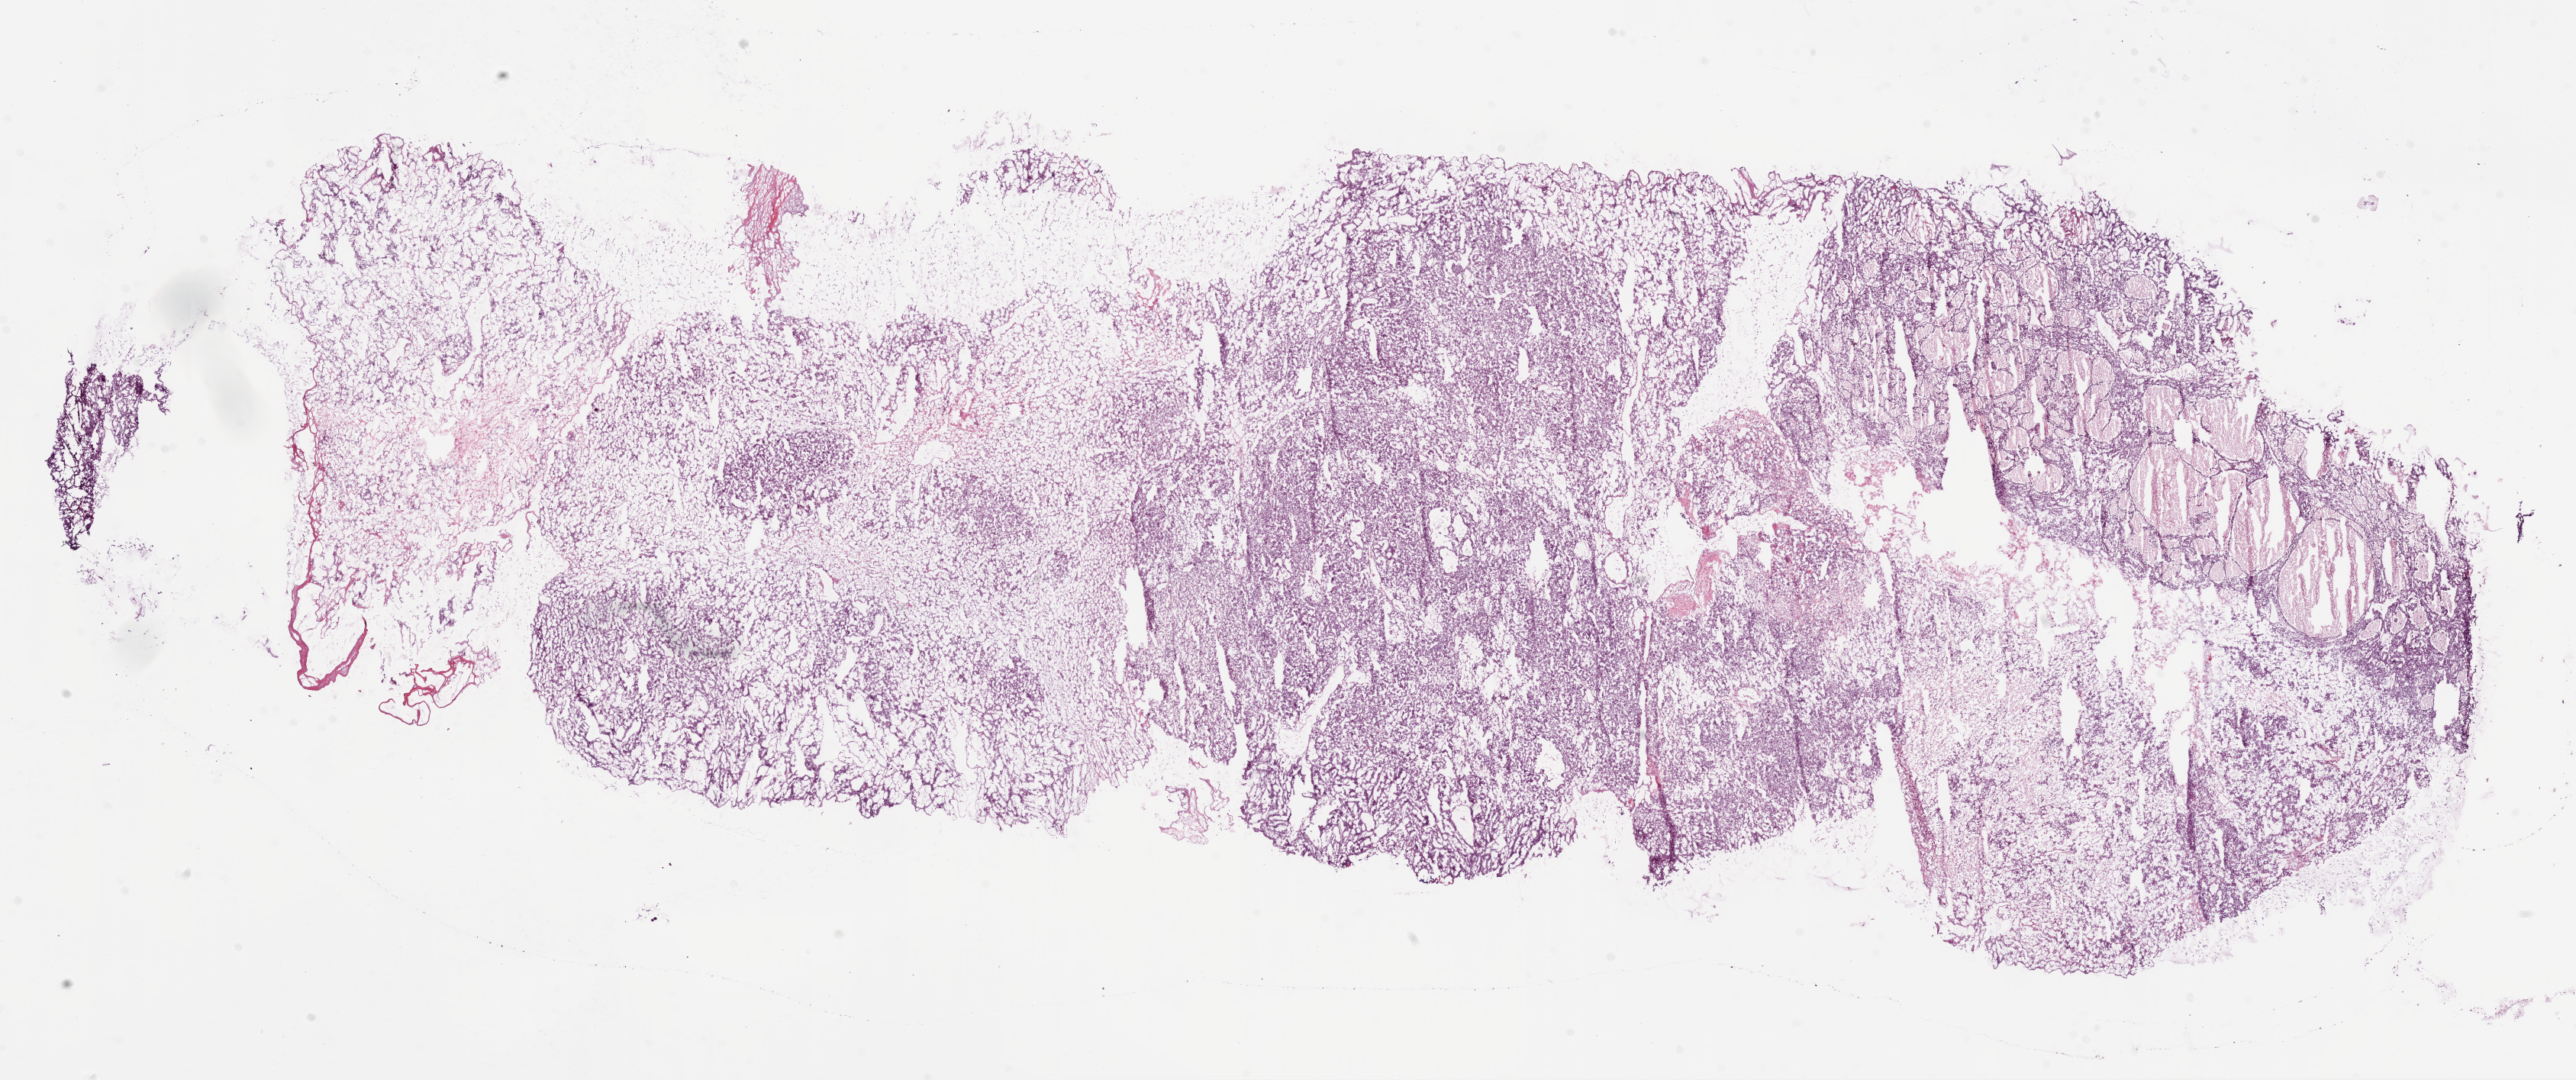
Digitized H&E tissue section (whole slide) — whole scanned area (about 27.1 x 11.4 mm) shown as a low-resolution overview; frozen section; primary tumour sample from the kidney. Male patient; age at initial diagnosis 58 years. Histologic grade: G3 (poorly differentiated). Slide review estimates, as recorded: tumour cells 85%, tumour nuclei 85%, normal cells 0%, stromal cells 15%, necrosis 0%.
* diagnosis: Clear cell adenocarcinoma, NOS
* AJCC pathologic stage: III (7th edition)